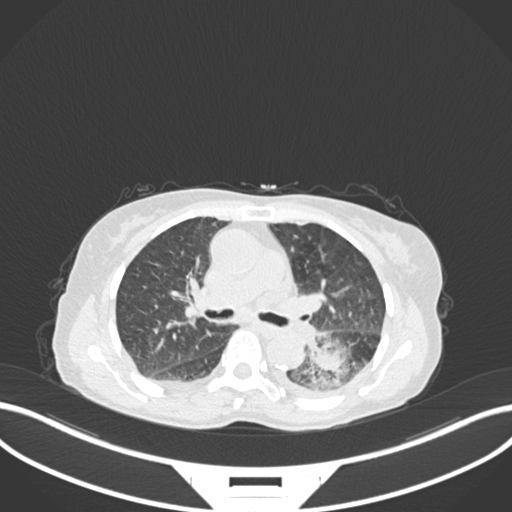
Chest CT, one axial slice; position 106 of 233 along the scan axis; reconstruction kernel B30f; 120 kVp; lung window (W 1500 / L -600 HU); 1 mm slice thickness; 512 × 512 image matrix, field of view 400 × 400 mm. Female patient, age 78 years. From the clinical record (not read from this slice): clinical TNM (as recorded): T3 N0 M1.
Outlined on this slice (bounding box drawn by a radiologist):
- lung tumour (recorded histology: squamous cell carcinoma): box from (x=294, y=326) to (x=358, y=393) px